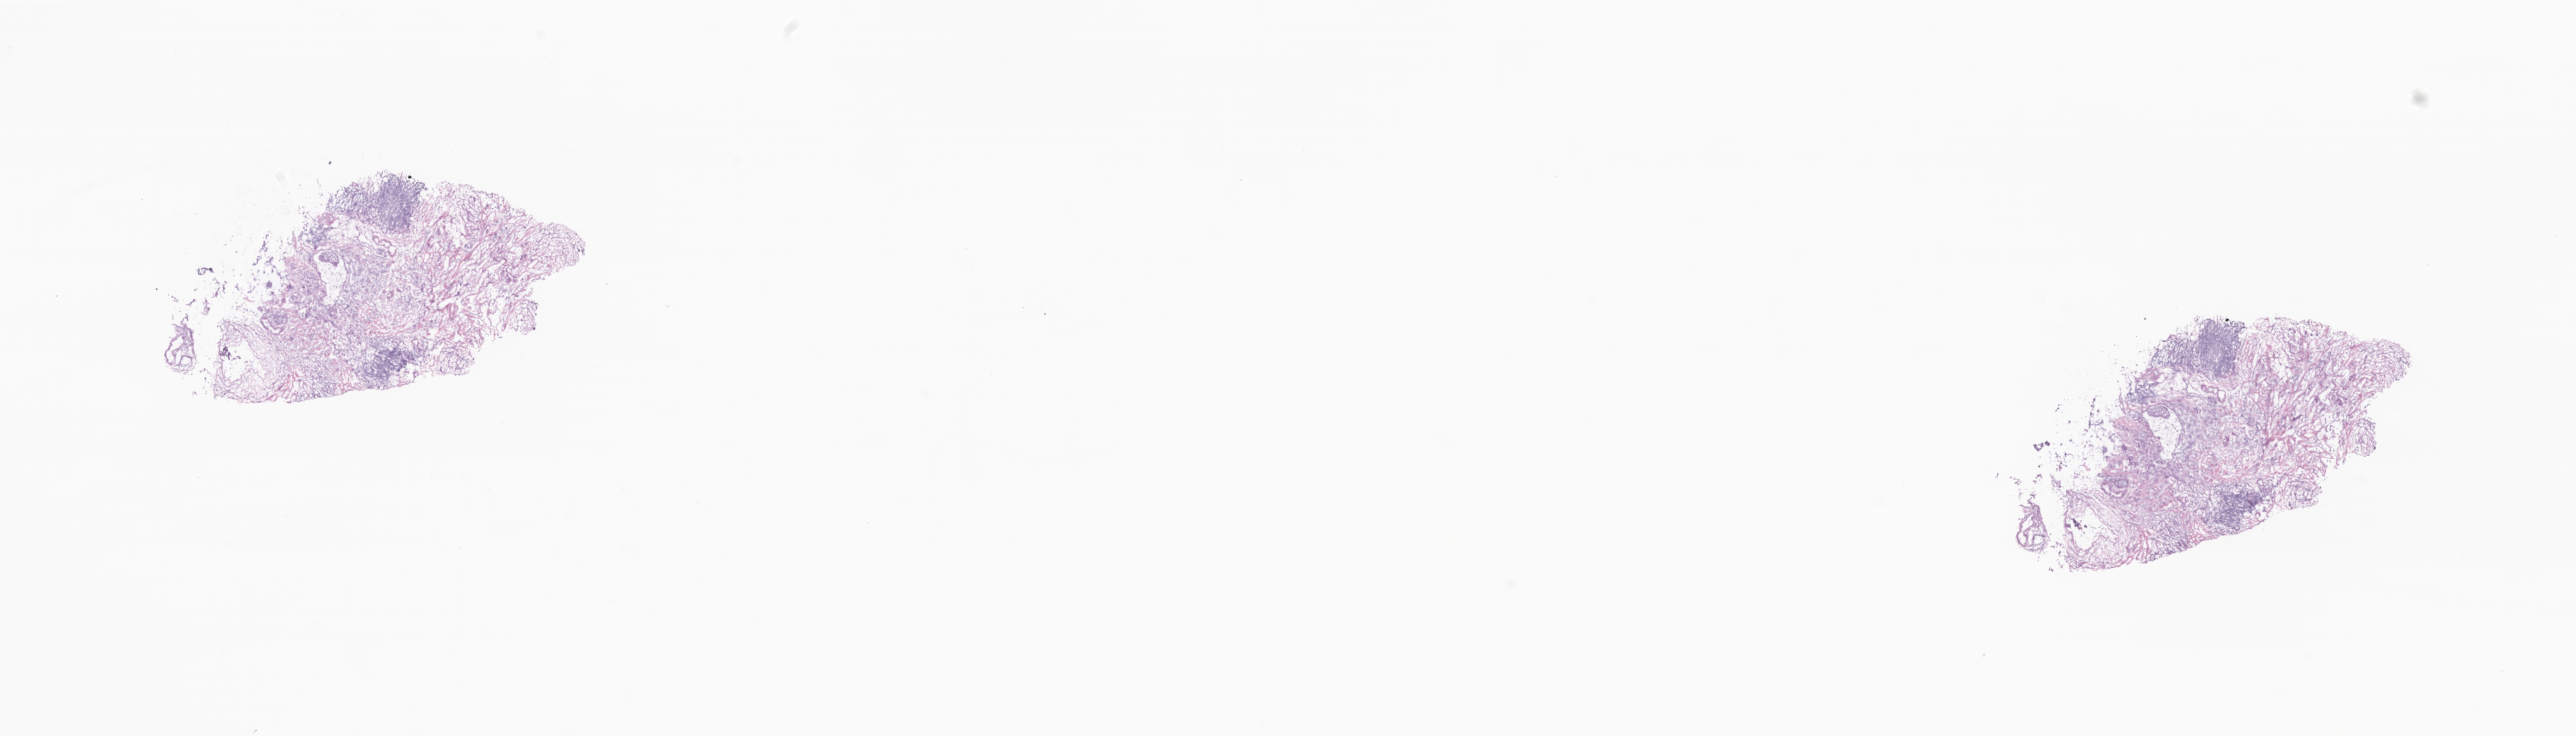
Whole-slide image, haematoxylin and eosin stain, shown as a low-resolution overview of the whole scanned area (about 28.9 x 8.2 mm); frozen section (tissue freezing medium); primary tumor; site: breast (right). Patient: female, age at initial diagnosis 41 years. Slide review estimates, as recorded: tumor cells 30%, tumor nuclei 40%, stromal cells 50%, necrosis 0%, normal cells 20%. Infiltration values recorded for this section: lymphocyte infiltration 0%, monocyte infiltration 0%, neutrophil infiltration 0%.
• histologic diagnosis: Infiltrating duct carcinoma, NOS
• section: bottom of the tissue portion